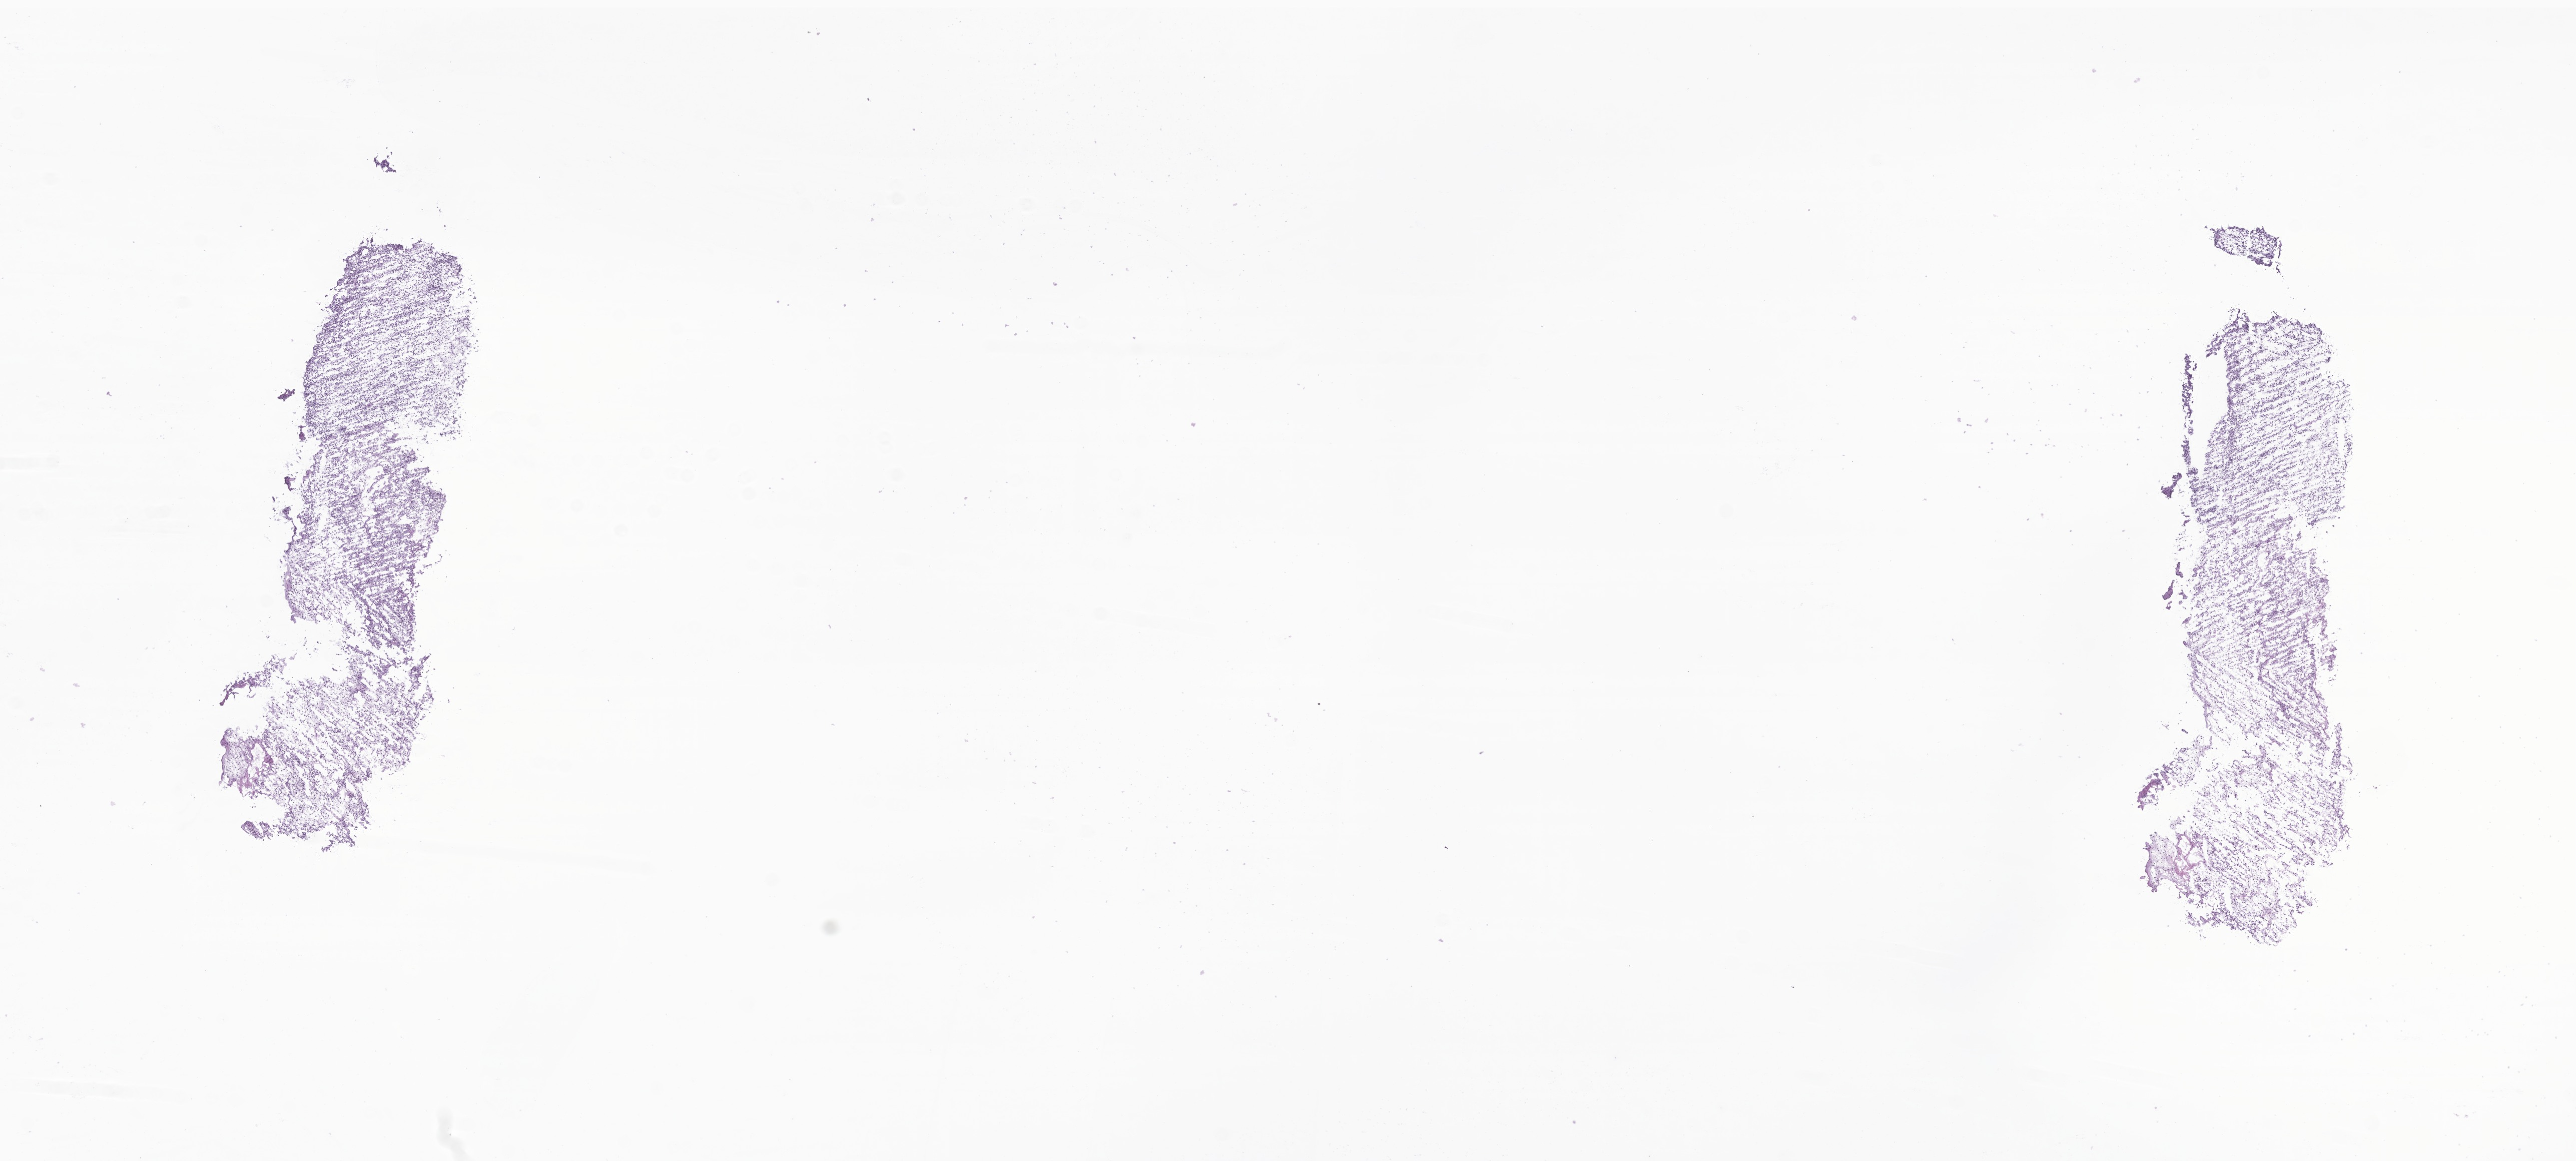
Digitized H&E-stained section of tumor tissue from the nasopharynx — a low-resolution overview of the entire scanned area, about 21.7 x 9.8 mm; cryosection (OCT / tissue freezing medium). Patient: male, age 54 months.
• diagnosis (ICD-O-3 morphology term): Embryonal rhabdomyosarcoma, NOS